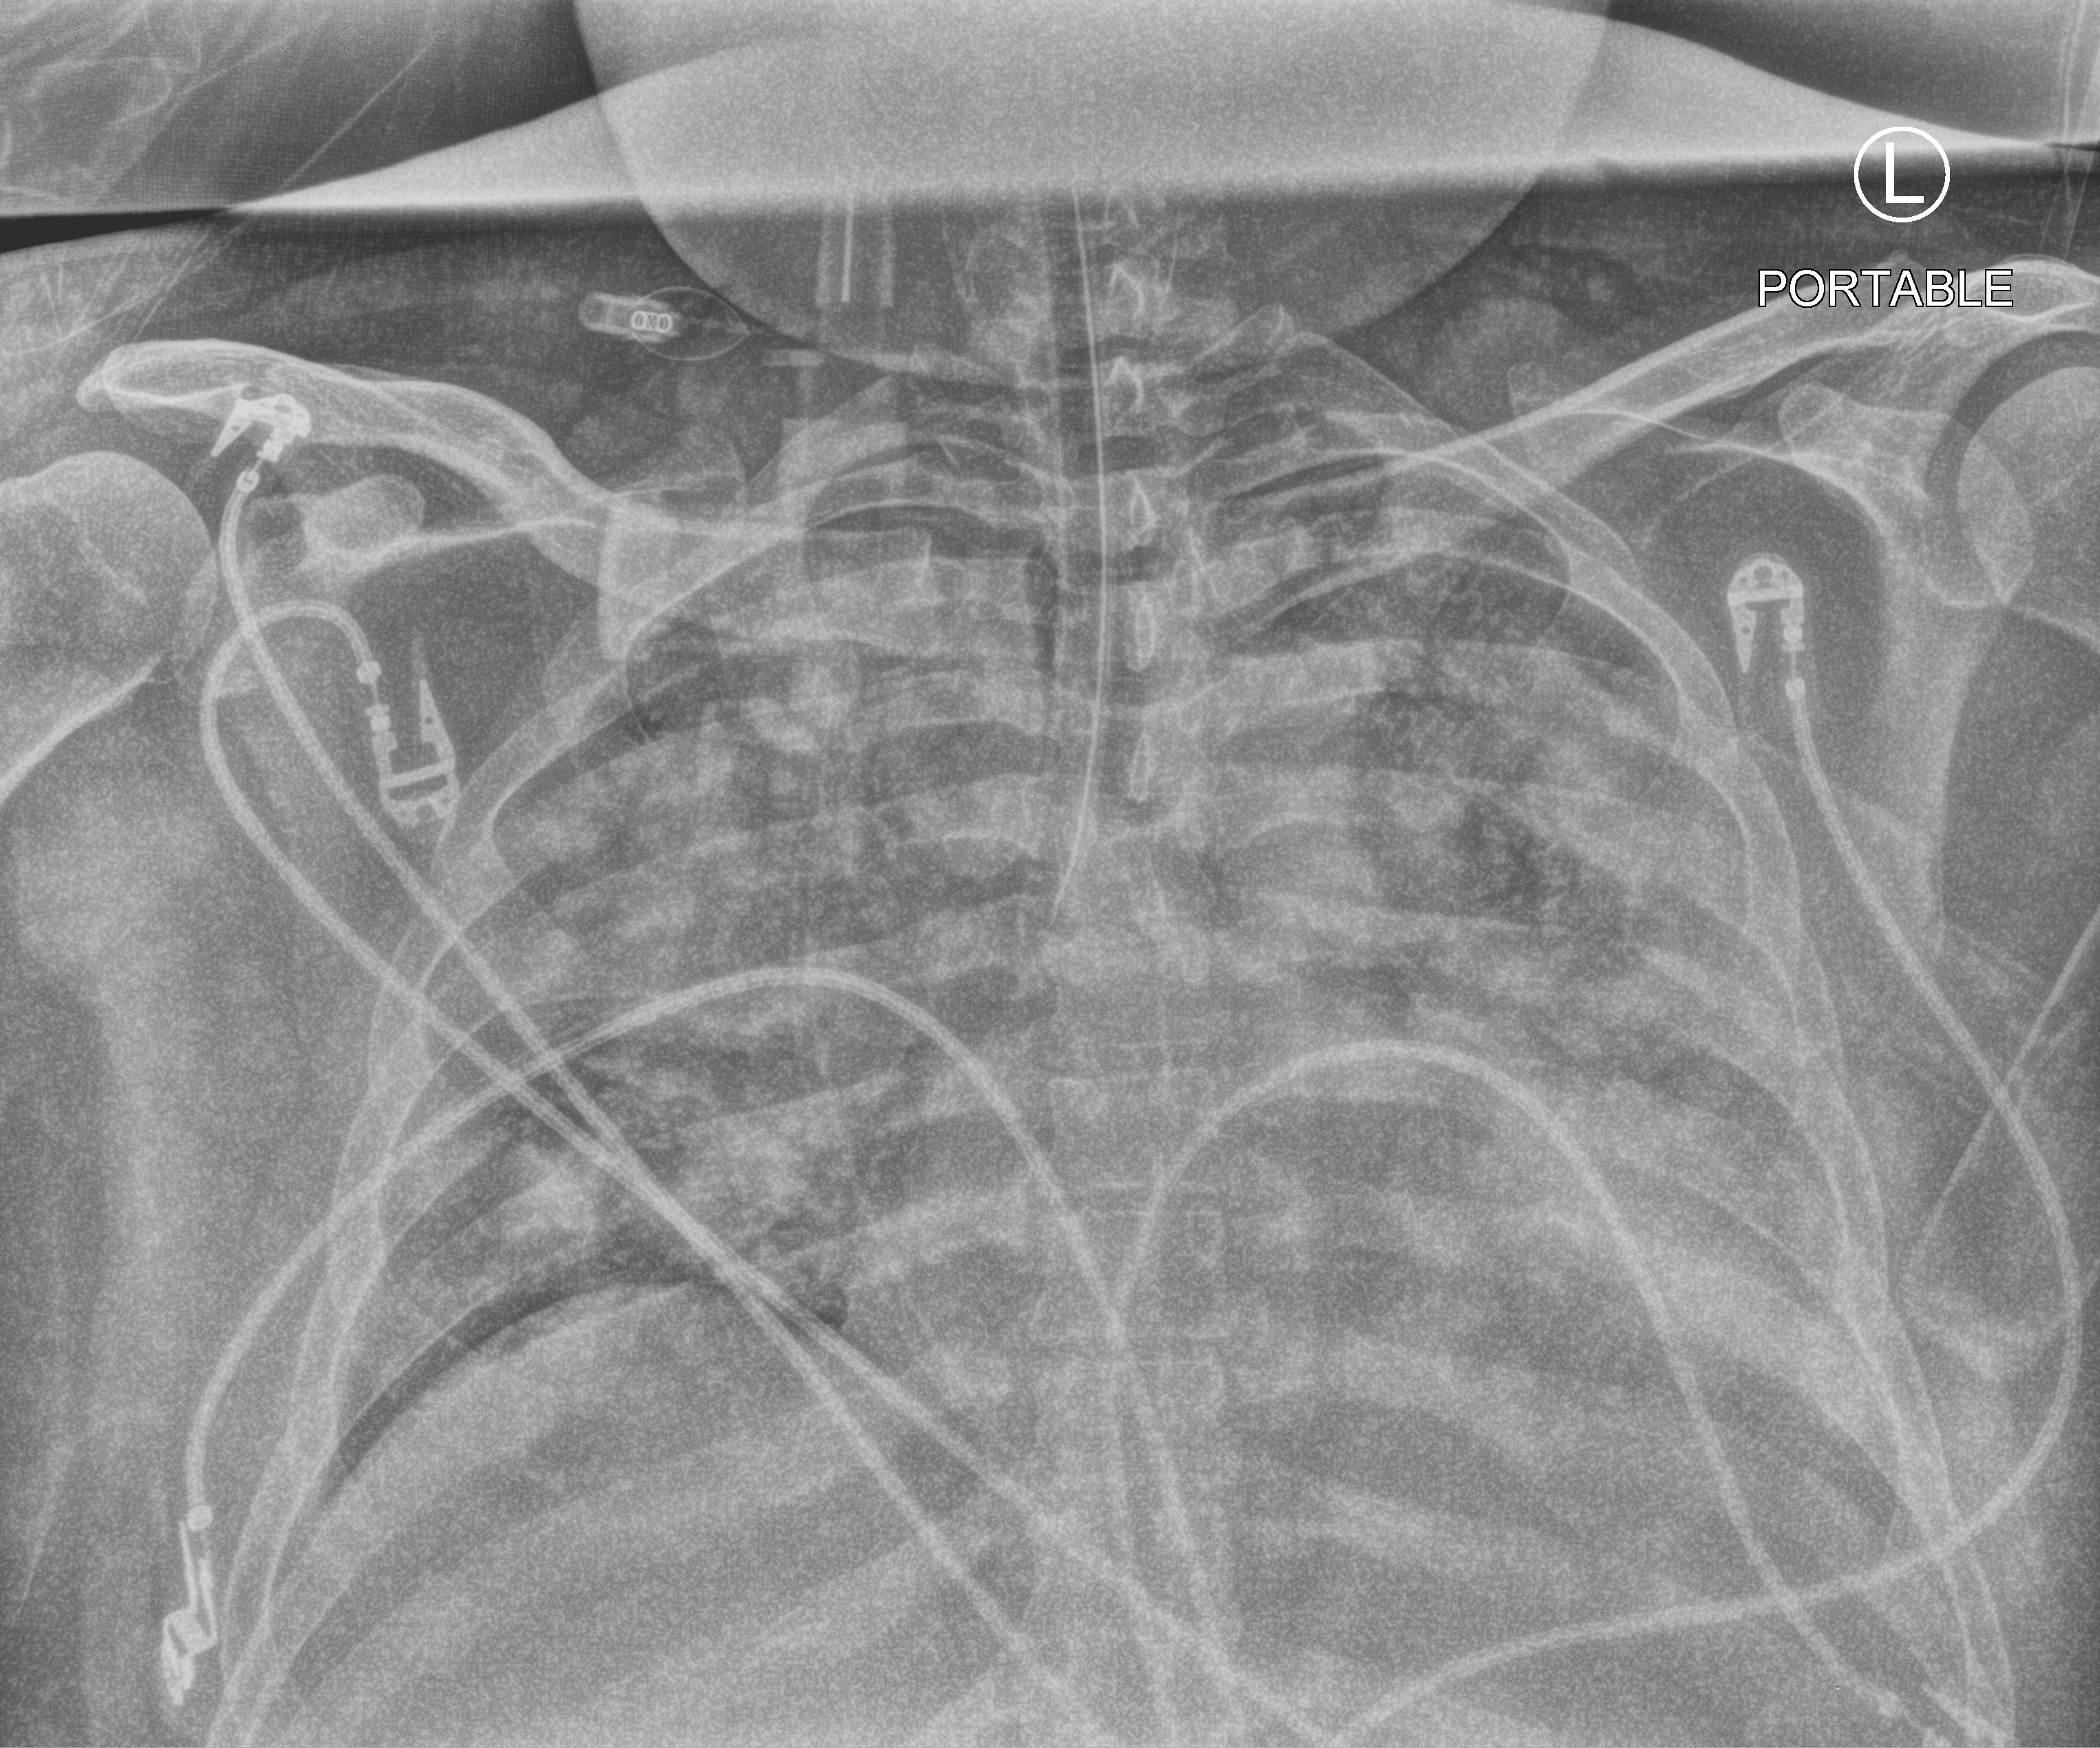
Portable chest radiograph. Patient hospitalised with COVID-19, aged 18–59 years.
Hospital-stay facts (about this admission, not read from this image; timing relative to this image not recorded): chronic kidney disease (admission record): no.